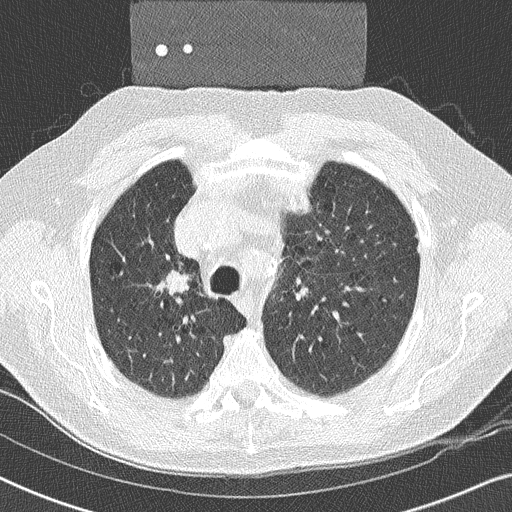
Low-dose screening chest CT, axial slice; second annual screen; lung window (W 1500 / L -600 HU); 2 mm slice thickness; lung (sharp) reconstruction kernel (B50f). Male participant, aged 59 years at enrolment. Former smoker at enrolment.
Lesion marked by an expert reader, bounding box <149,258,206,307> (left, top, right, bottom; pixels). Reader record for this screening exam (exam-level; its link to the box is not recorded): non-calcified nodule or mass ≥4 mm, right upper lobe, 17 × 16 mm, smooth margins, soft tissue attenuation, pre-existing on the prior screen: yes.